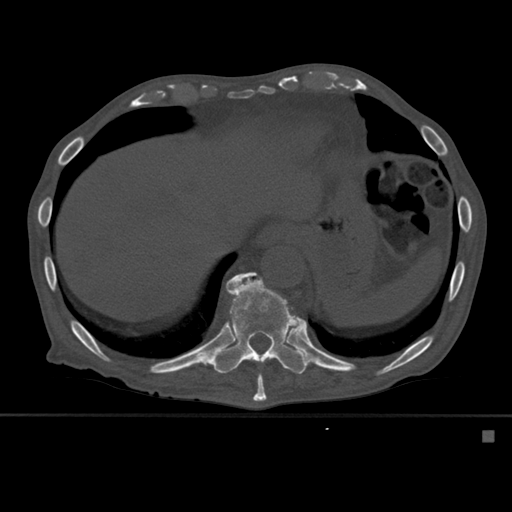
CT including the spine, one axial slice. Position 302 of 527 along the scan axis. Bone window (W 1800 / L 400 HU). 512 × 512 image matrix. Patient: male, 78 years. From the clinical record (not read from this slice): primary cancer: prostate.
Annotated regions visible in this slice (semi-automatically segmented with operator editing):
- T10 vertebra: box from (x=231, y=273) to (x=267, y=402) px
- T11 vertebra: (x=211, y=272)–(x=312, y=374)